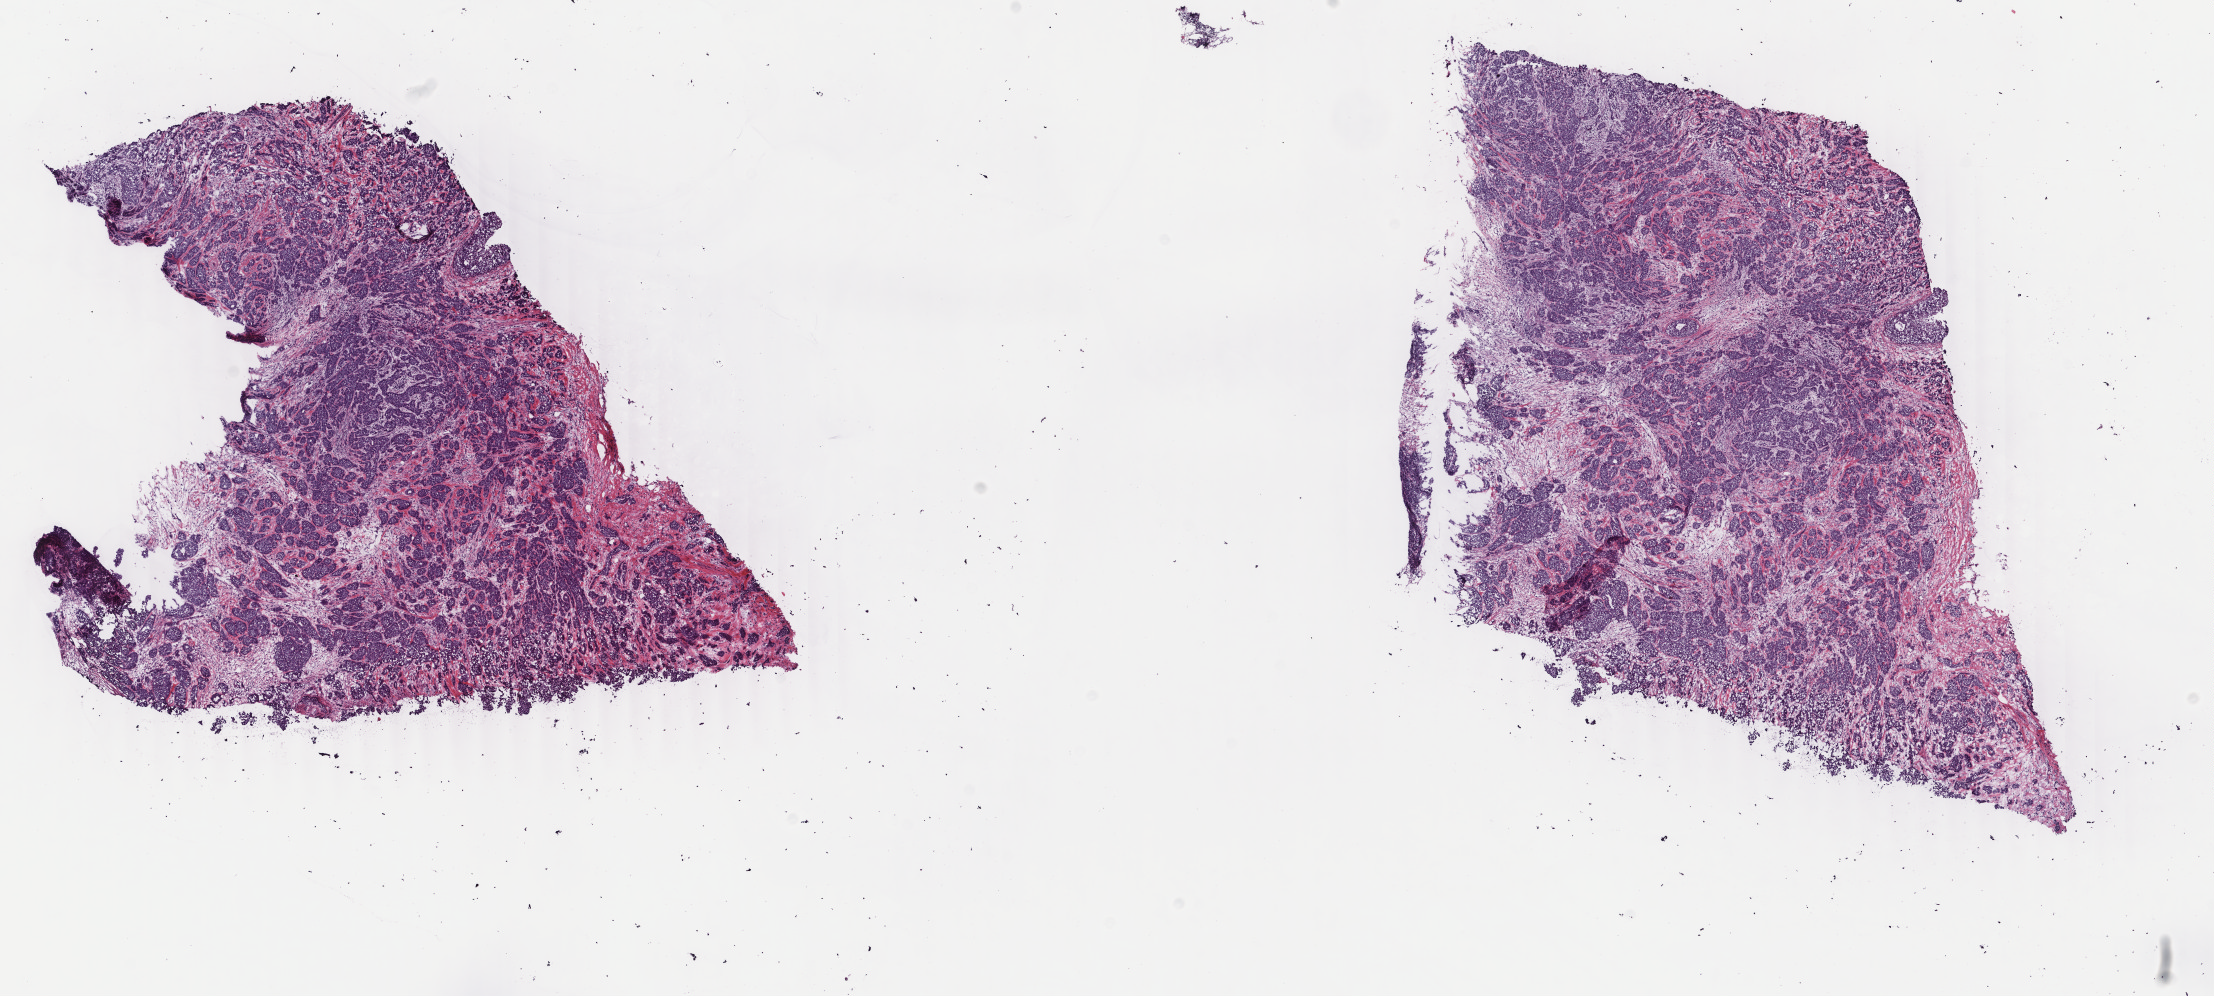
Whole-slide histology image, H&E-stained — whole scanned area (about 17.6 x 7.9 mm, acquisition: 40x scan) shown as a low-resolution overview. Frozen section. Breast, primary tumour sample. Female, age 46 years at initial diagnosis. Pathologist review of this section (percent, as recorded): tumour cells 75%, tumour nuclei 75%, normal cells 0%, stromal cells 25%, necrosis 0%. Infiltration values recorded for this section: lymphocyte infiltration 3%, monocyte infiltration 1%, neutrophil infiltration 1%.
AJCC pathologic stage: IIA (6th edition). TNM: T2 N0 M0. Pathologic diagnosis: Infiltrating duct carcinoma, NOS.